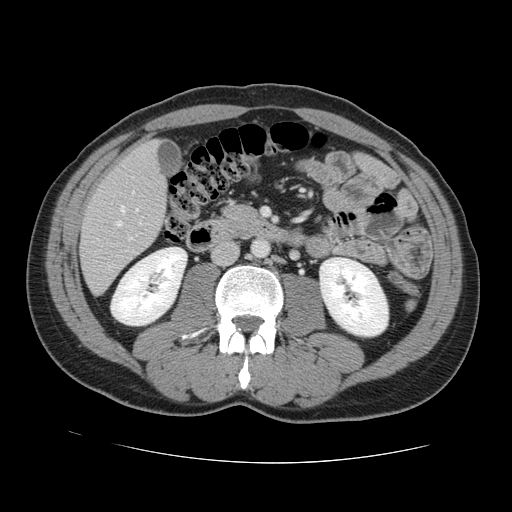
Contrast-enhanced abdominal CT, one axial slice. Slice 40 of 131 in the series (ordered by position). 120 kVp. Intravenous contrast given. Soft-tissue window (W 400 / L 40 HU). 2.5 mm slice thickness. 512 × 512 image matrix, field of view 380 × 380 mm. Male patient, age 40 years. From the clinical record (not read from this slice): diagnosis: colorectal cancer liver metastases, imaged before liver resection; multiple liver metastases: yes; largest metastasis: 2.9 cm.
Outlined on this slice (expert manual segmentation):
- hepatic veins: bounding box <117,207,141,226> (left, top, right, bottom; pixels)
- liver: <82,143,166,293>
- planned liver remnant (the part of the liver to remain after resection): <134,143,156,163>
- portal vein (with intrahepatic branches): <129,191,134,240>